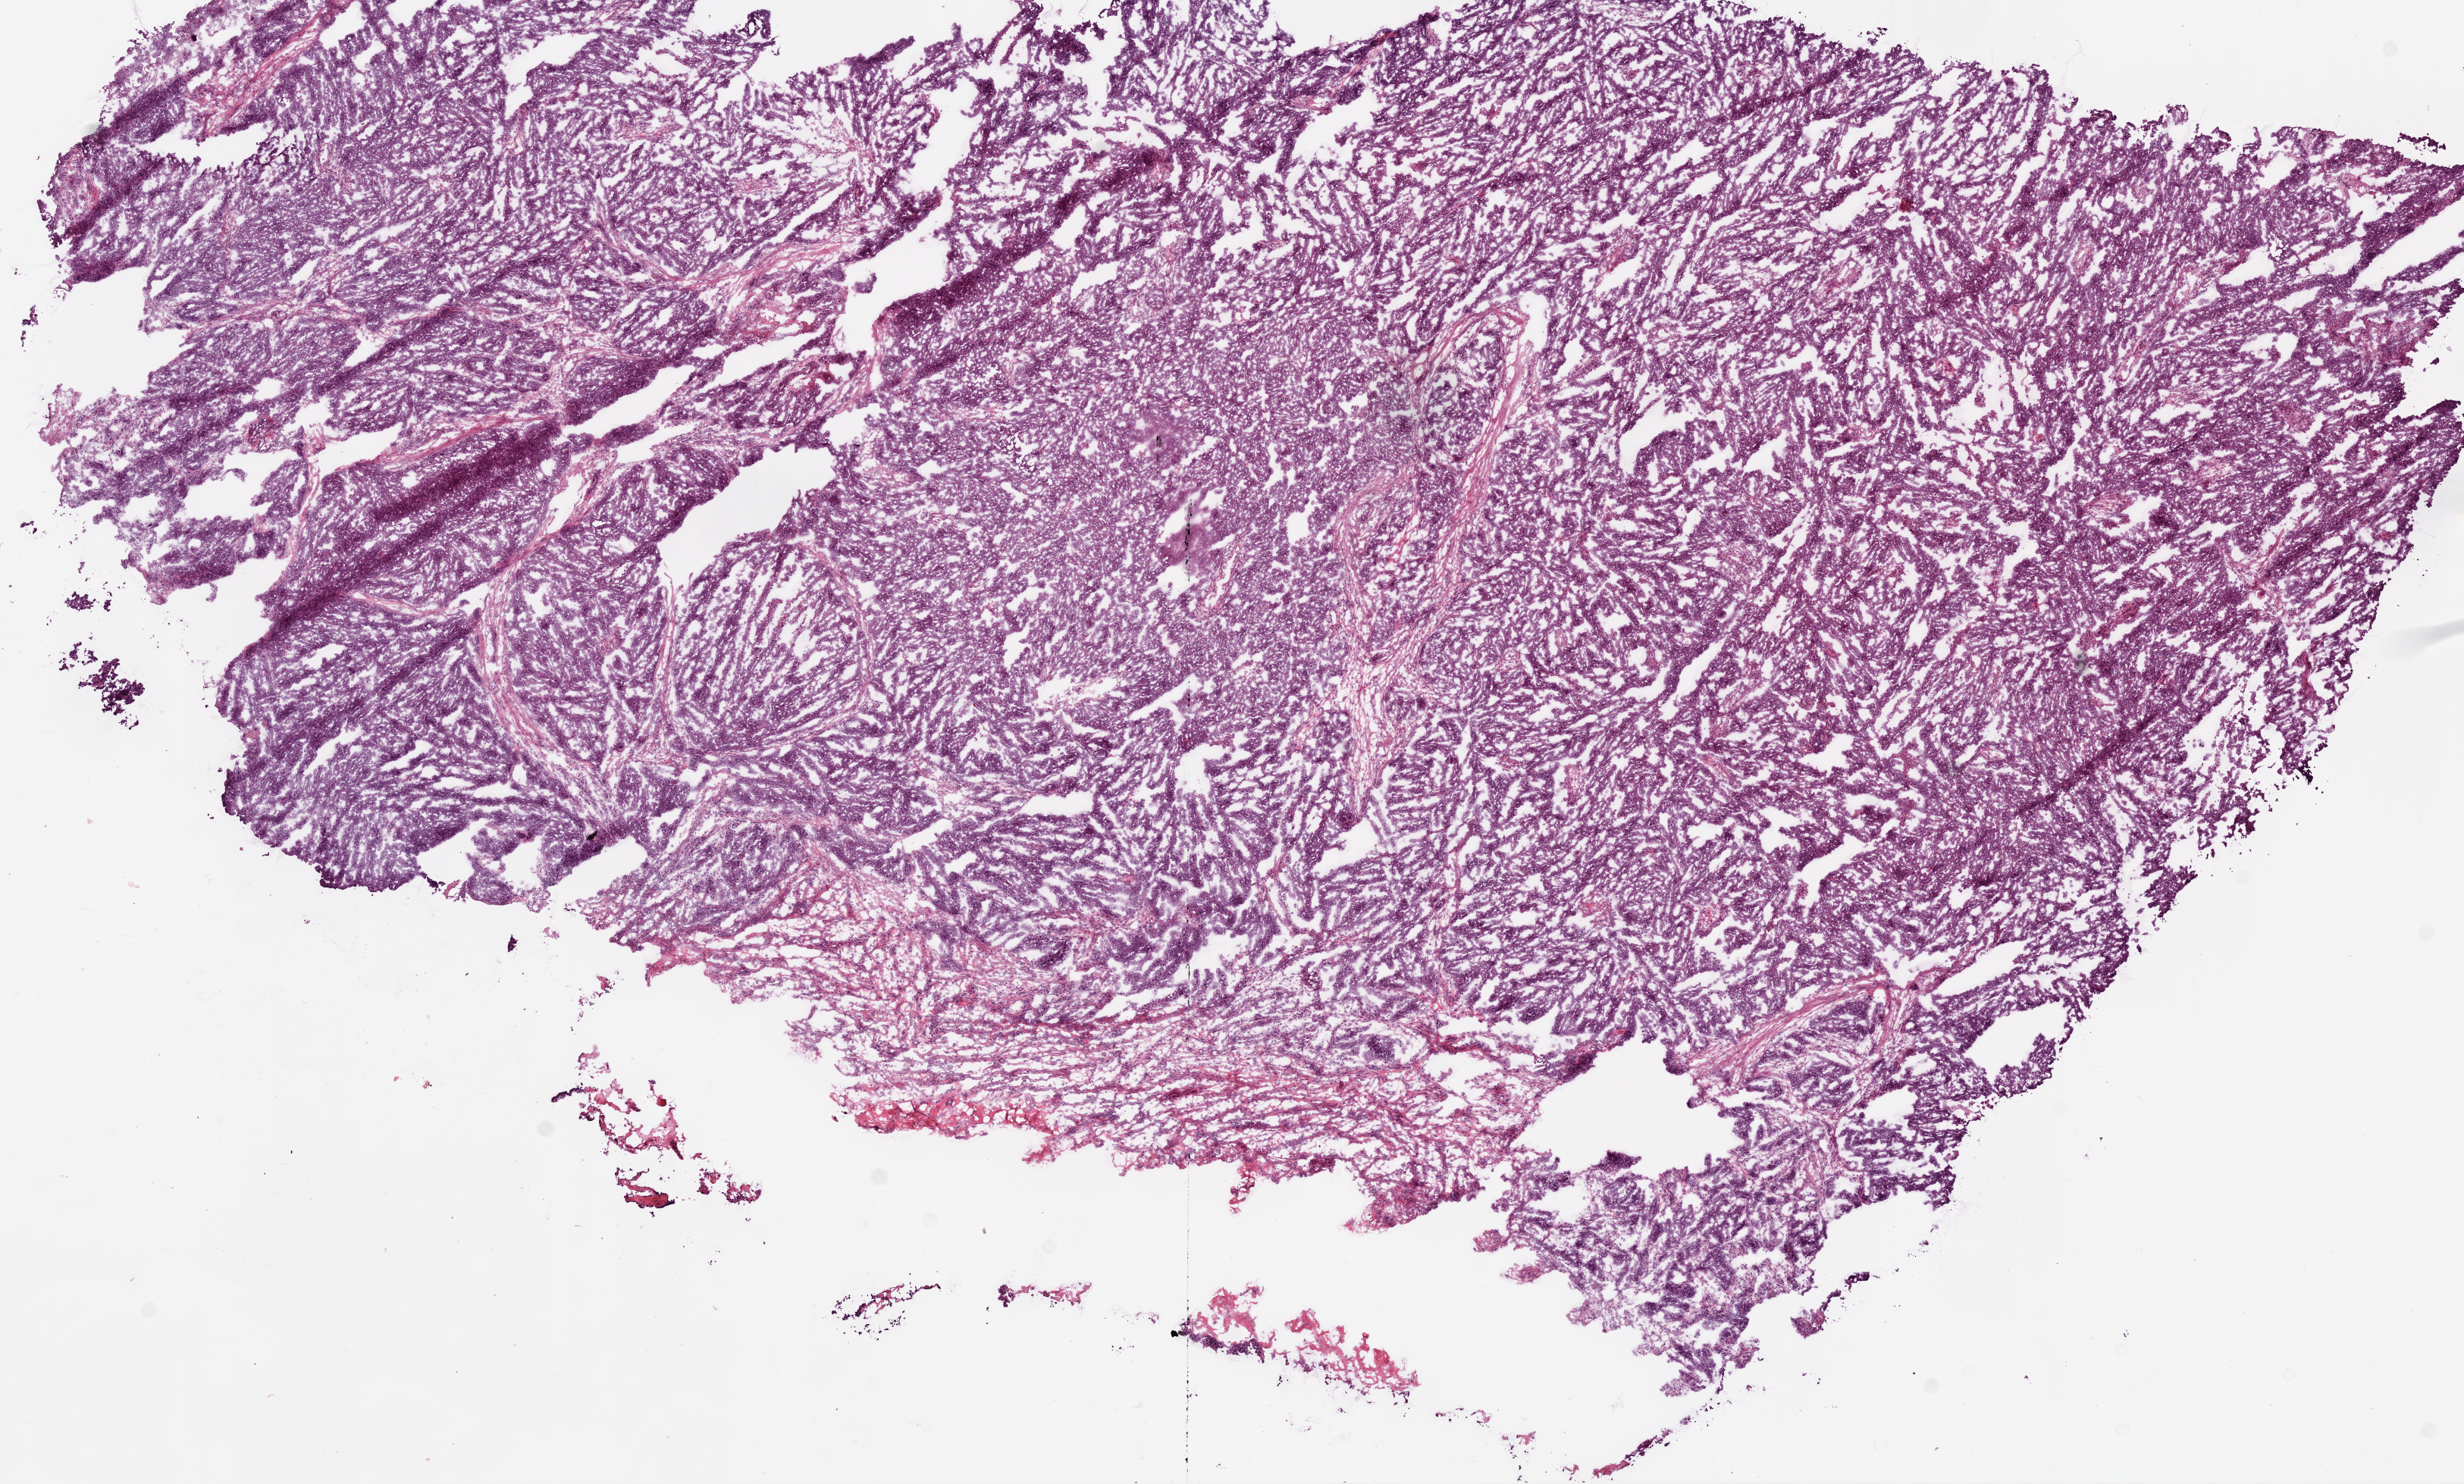
H&E-stained whole-slide image — a low-resolution overview of the entire scanned area, about 13.0 x 7.9 mm (slide scanned at 20x), frozen section from the bottom of the tissue portion, primary tumour sample from the ovary. Female patient; age at initial diagnosis 73 years. Histologic grade: G3 (poorly differentiated). Slide review estimates, as recorded: tumour cells 94%, tumour nuclei 95%, normal cells 0%, stromal cells 5%, necrosis 1%.
* pathologic diagnosis: Serous cystadenocarcinoma, NOS
* FIGO stage: IIIC